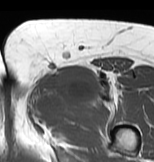
MRI of an extremity soft-tissue mass, one axial slice. Position 43 of 83 along the scan axis. MR volume resampled by the dataset authors to the PET/CT grid (not the native acquisition matrix). 154 × 162 image matrix, field of view 150 × 158 mm. Female patient. From the clinical record (not read from this slice): histological type: myxofibrosarcoma; grade: intermediate; site of the primary tumour: left thigh.
Annotated regions visible in this slice (expert contour drawn on MRI and transferred to this co-registered scan by the dataset authors):
- gross tumour volume including surrounding oedema: box from (x=26, y=68) to (x=123, y=119) px
- gross tumour volume (mass): (x=44, y=68)–(x=97, y=103)